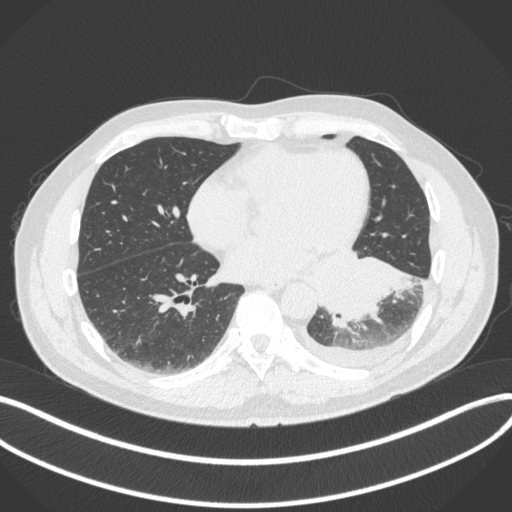
Chest CT, one axial slice. Position 143 of 350 along the scan axis. Lung window (W 1500 / L -600 HU). 1 mm slice thickness. 512 × 512 image matrix, field of view 400 × 400 mm. Male patient, age 58 years. From the clinical record (not read from this slice): clinical TNM (as recorded): T3 N1 M1b; histopathological grade: G3.
Annotated regions visible in this slice (rectangle marked by the reading radiologist):
- lung tumour (recorded histology: small cell carcinoma): bounding box [x1, y1, x2, y2] px = [315, 258, 419, 332]